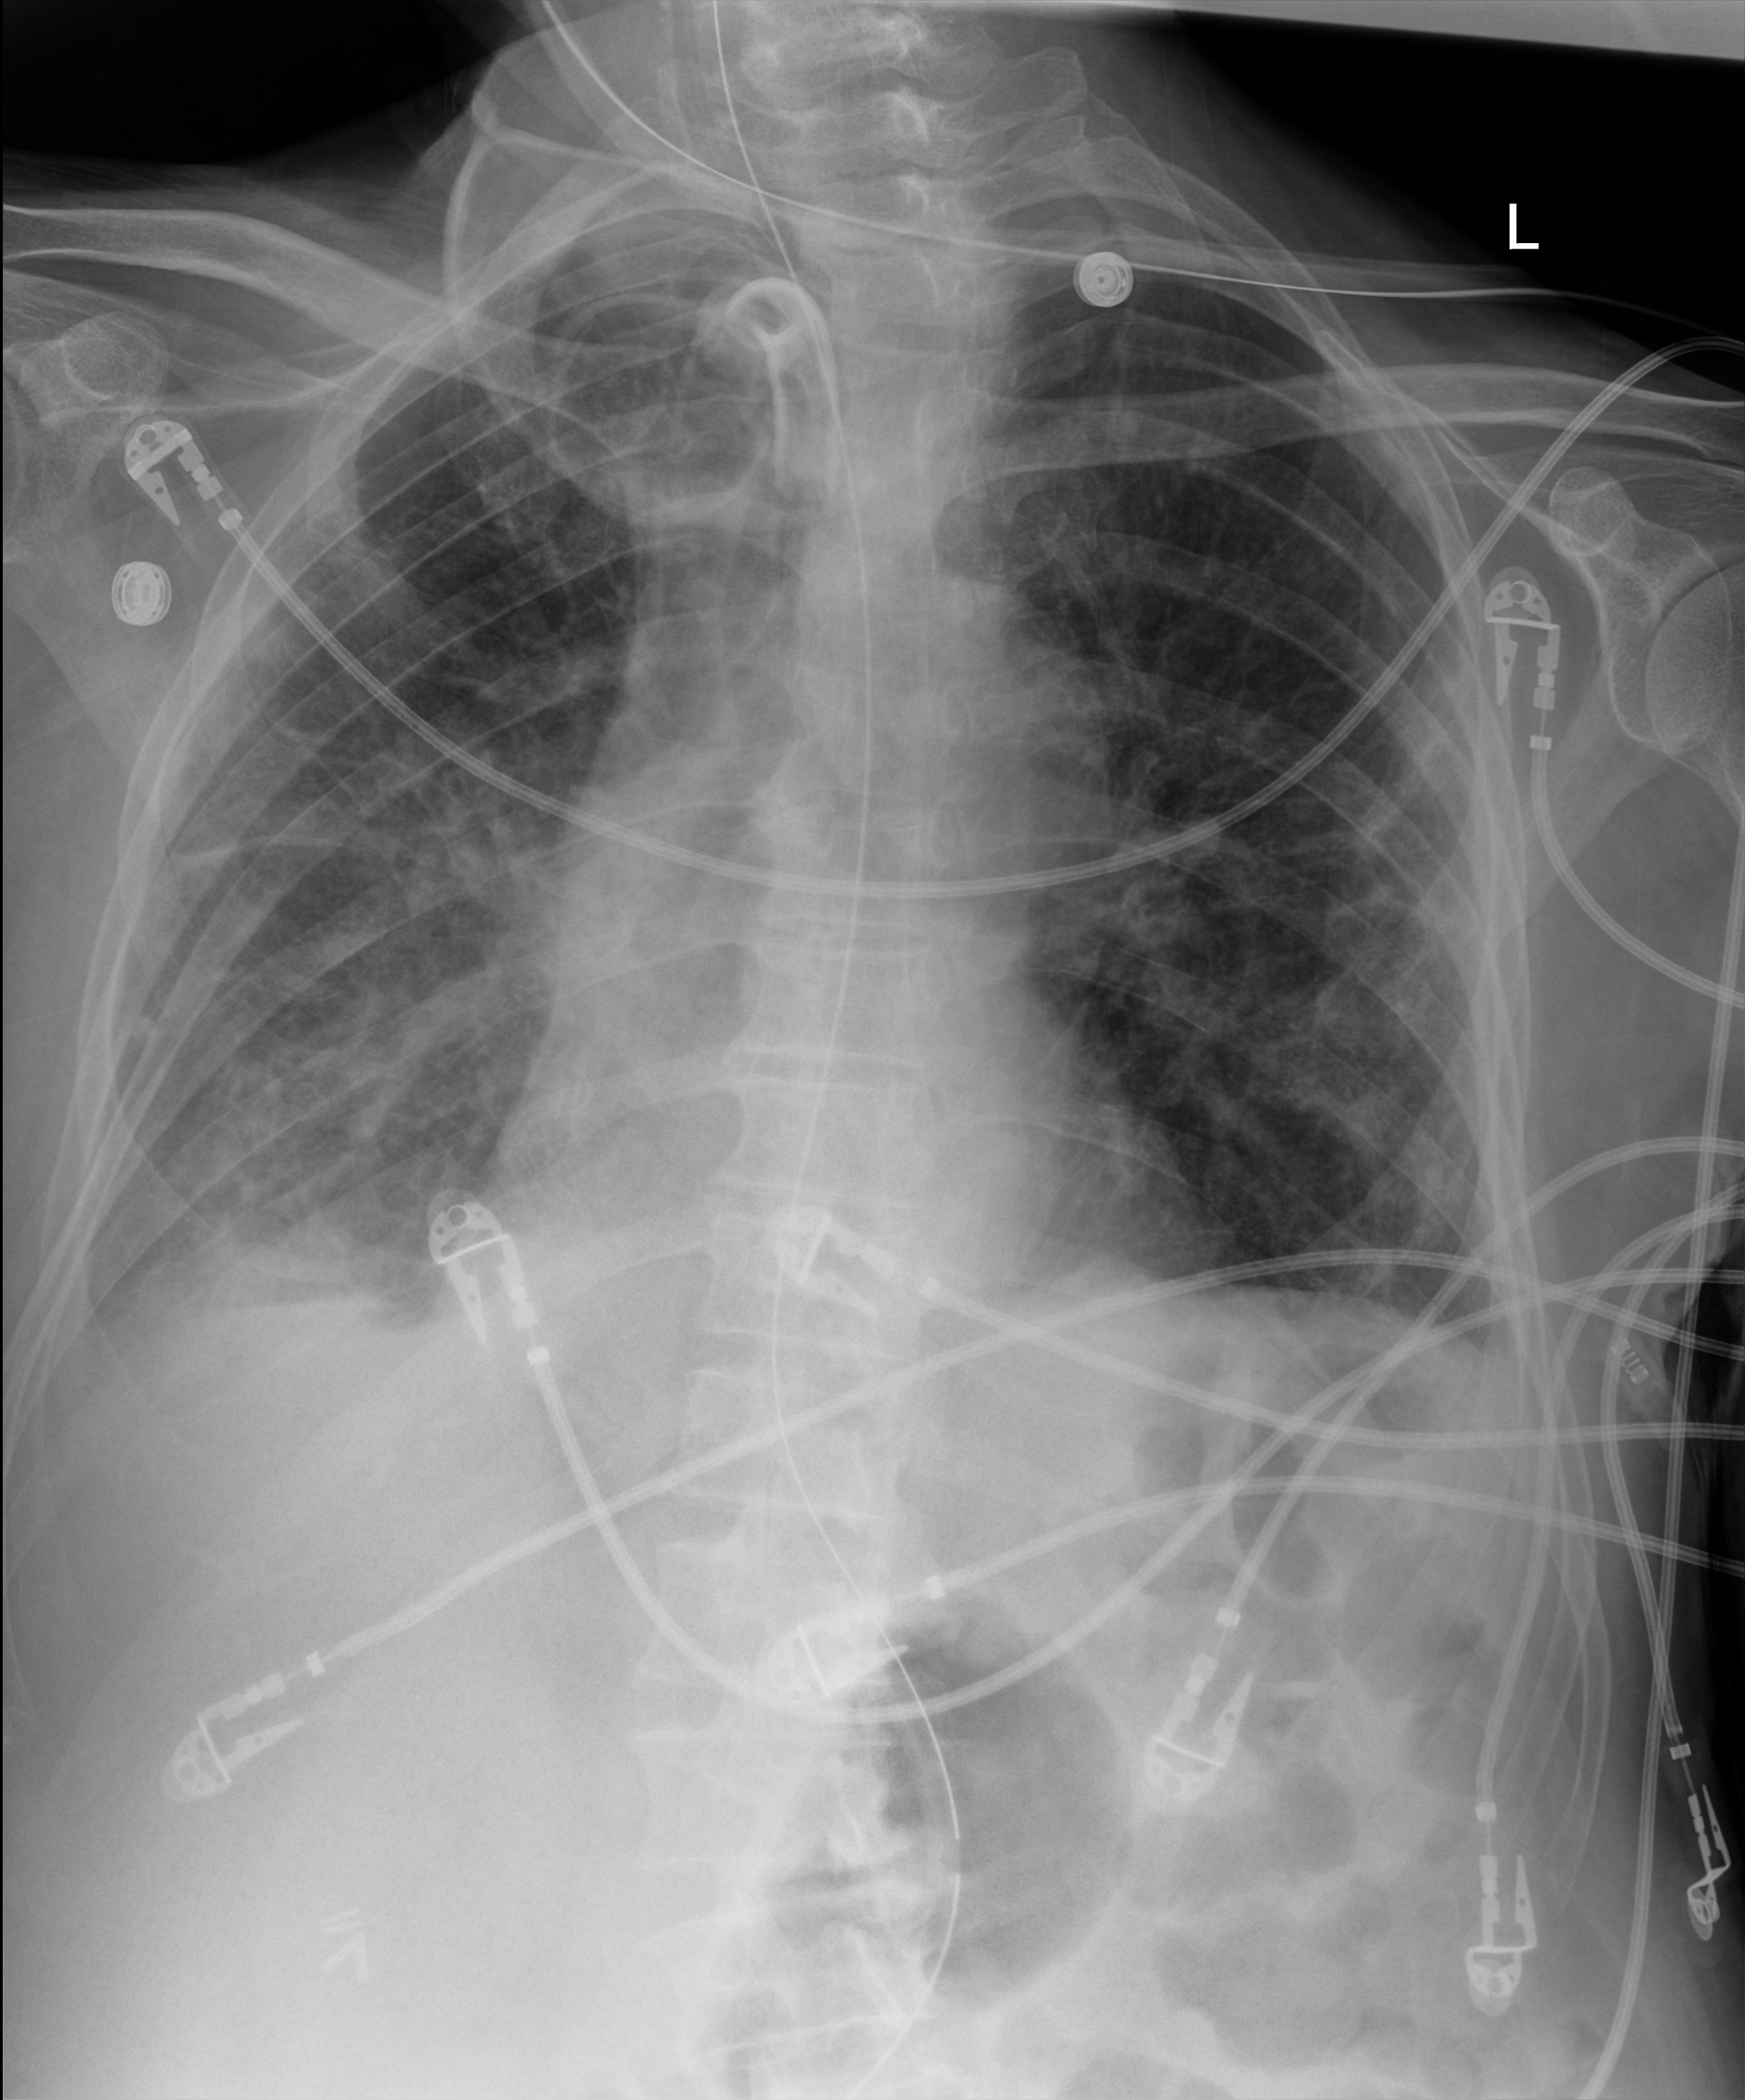
Bedside chest radiograph (digital radiography); anteroposterior (AP) projection. Patient hospitalised with COVID-19; male, aged 75–90 years.
Admission-level facts for this patient (not findings on this image; timing relative to this image not recorded): mechanically ventilated during this hospital stay: yes.